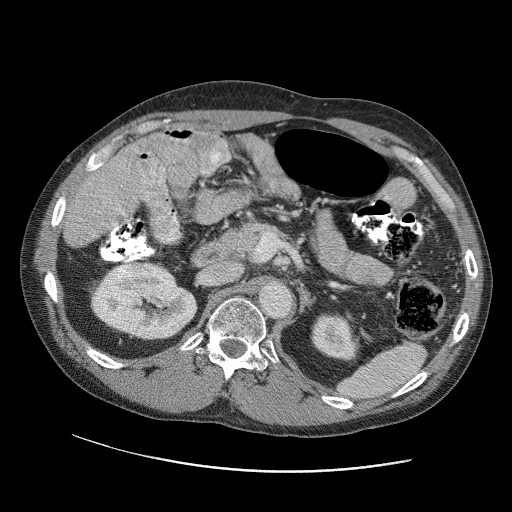
Contrast-enhanced abdominal CT (liver protocol), one axial slice; slice 52 of 109 in the series (ordered by position); reconstruction kernel STANDARD; soft-tissue window (W 400 / L 40 HU); 512 × 512 image matrix, field of view 400 × 400 mm. Case-level facts recorded for this patient, not image findings: diagnosis: hepatocellular carcinoma (patient treated with transarterial chemoembolisation; whether this scan precedes or follows treatment is not stated here); TNM stage (as recorded): Stage-IIIC; Child-Pugh class: B.
Structures marked on this image (semi-automatically segmented with operator editing):
- liver parenchyma outside the tumour (the mass and vessels are separate outlines, so this box may not span the whole liver): bounding box (x1, y1, x2, y2) in pixels: (124, 144, 136, 156)
- liver vessels: (125, 145, 136, 155)